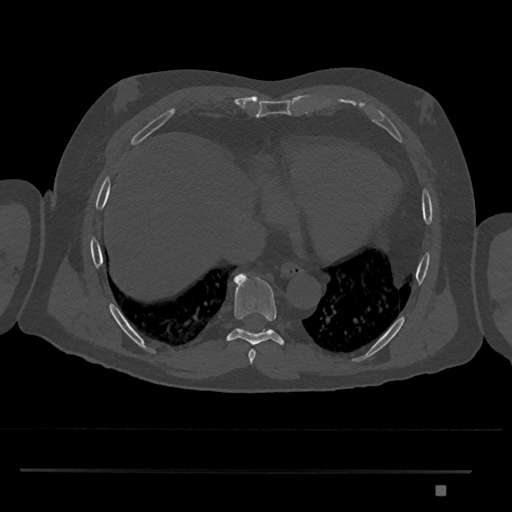
CT including the spine, one axial slice. Position 1108 of 1134 along the scan axis. Reconstruction kernel Br40s/3. 120 kVp. Bone window (W 1800 / L 400 HU). 512 × 512 image matrix, field of view 429 × 429 mm. Male patient, age 65 years. From the clinical record (not read from this slice): primary cancer: prostate.
Annotated regions visible in this slice (semi-automatically segmented with operator editing):
- T8 vertebra: bounding box [x1, y1, x2, y2] px = [227, 272, 284, 345]